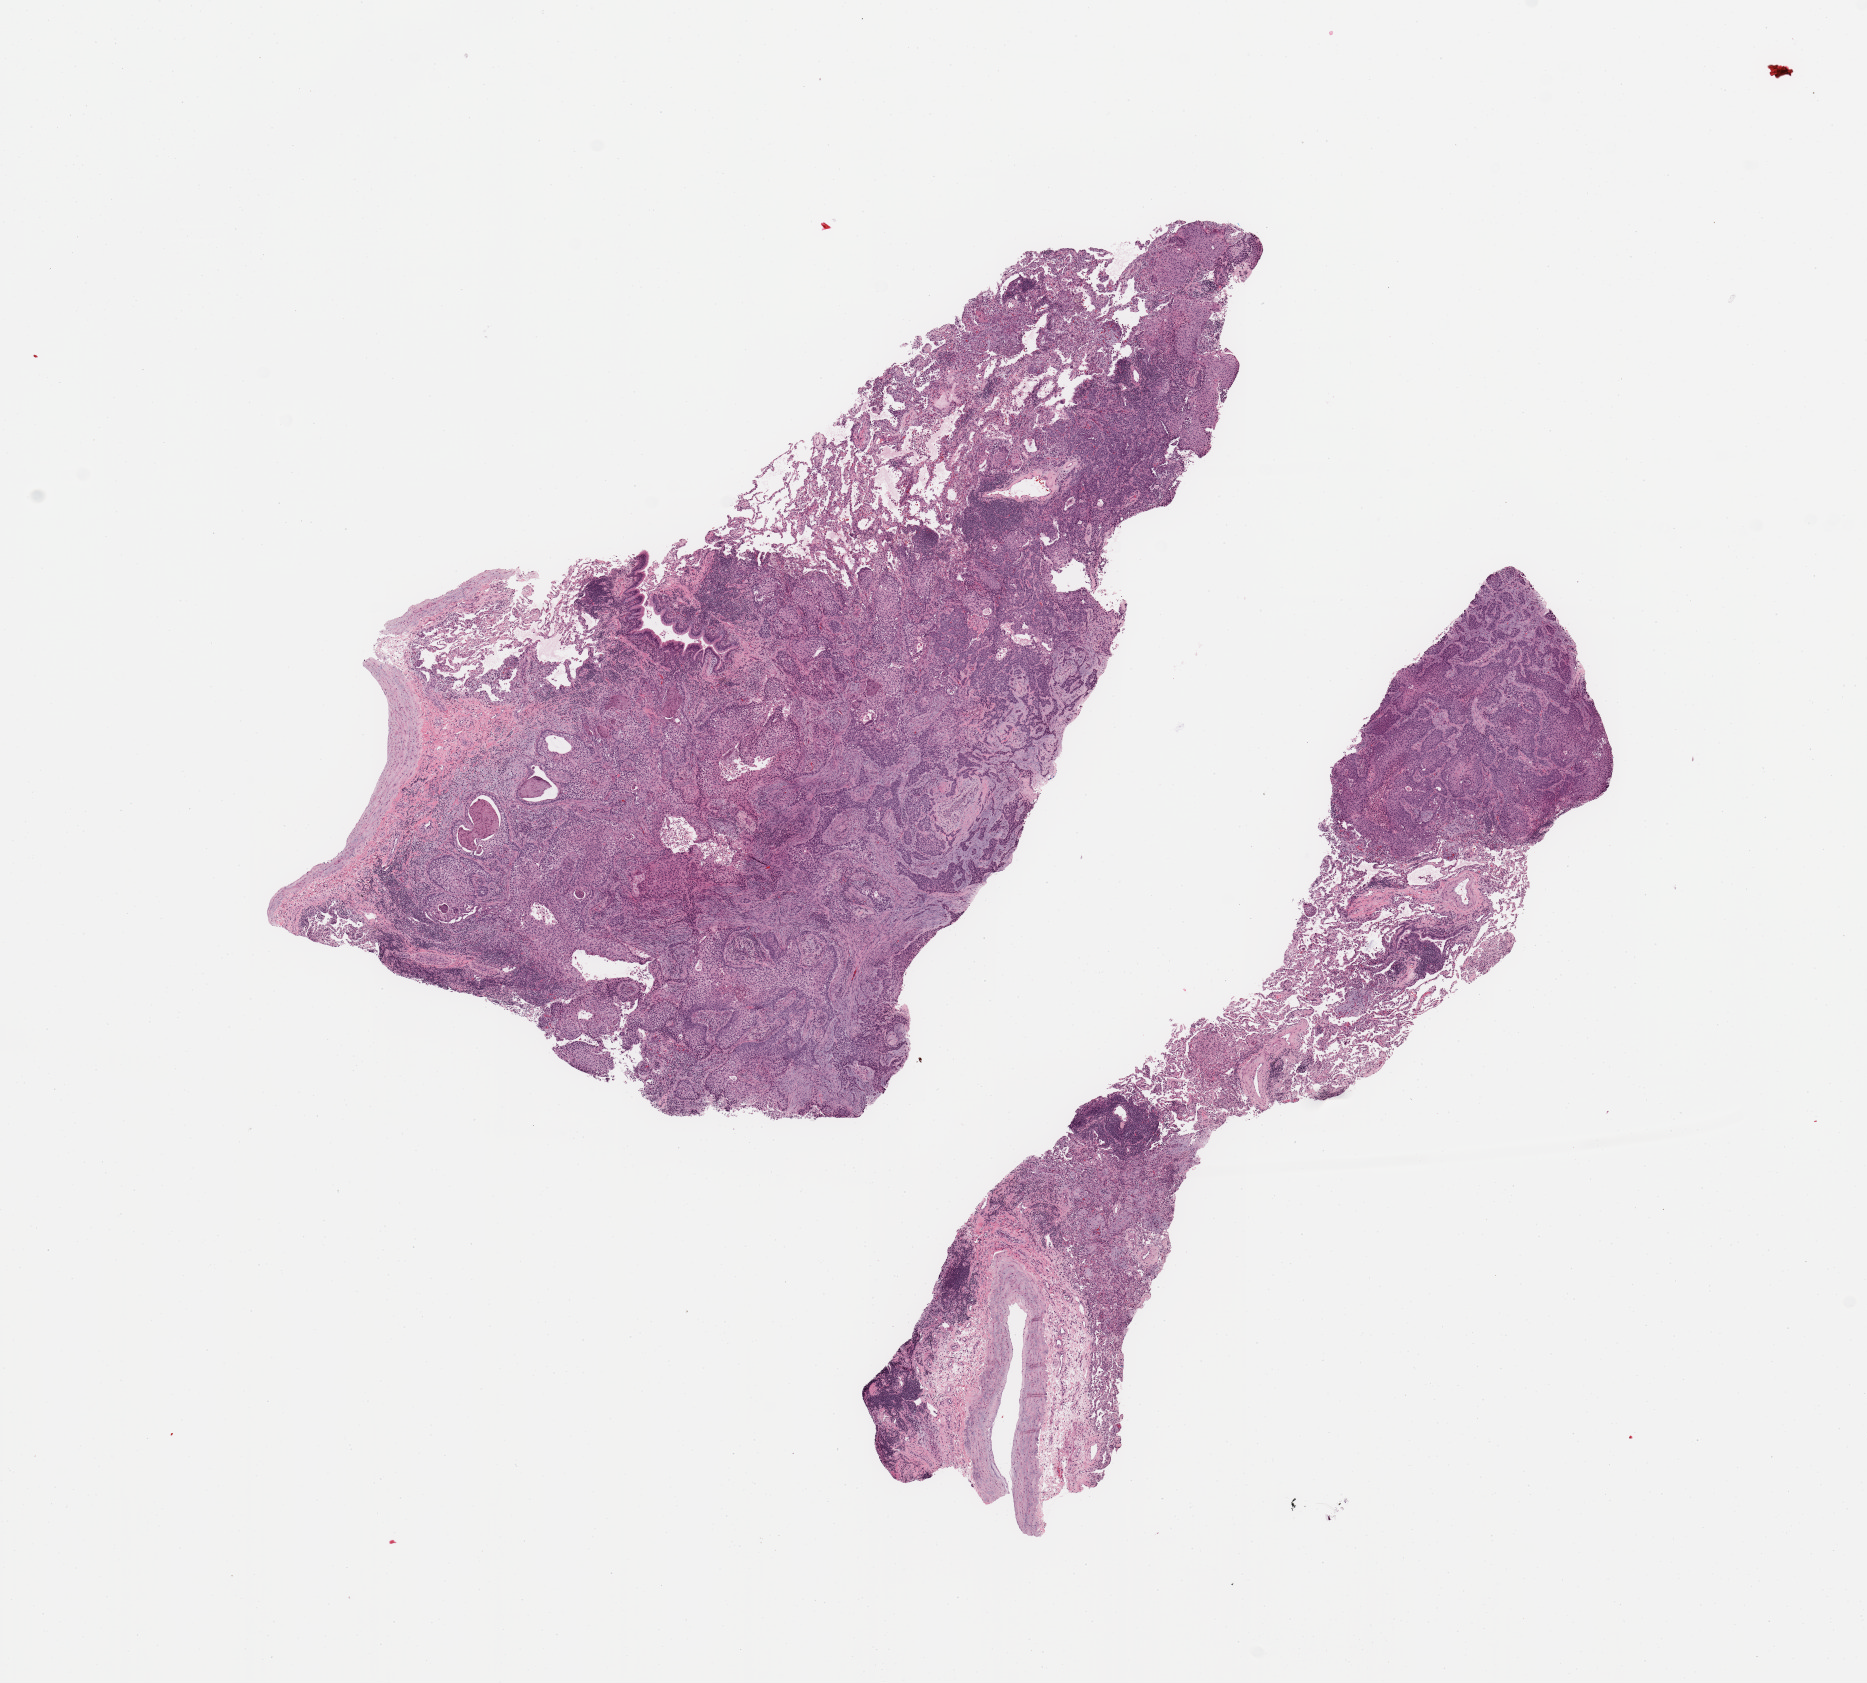
Whole-slide histology image, Hematoxylin and eosin (H&E) stained, whole scanned area (about 14.8 x 13.3 mm, acquisition: 20x scan) shown as a low-resolution overview; lung, tumour tissue. 75-year-old female patient.
Histologic diagnosis: Squamous cell carcinoma, NOS.